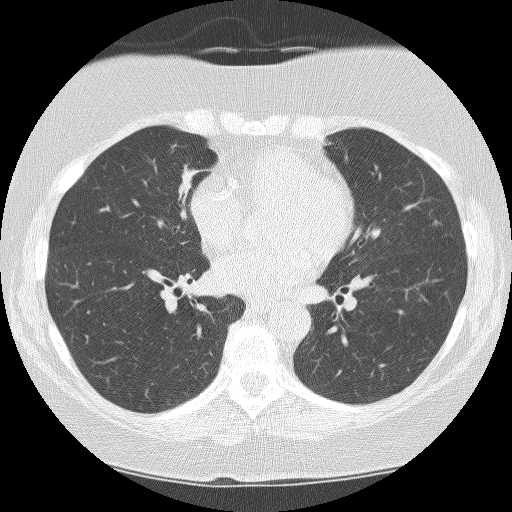
Low-dose screening chest CT, one axial slice; position 82 of 159 along the scan axis; 120 kVp; lung window (W 1500 / L -600 HU); 512 × 512 image matrix, field of view 299 × 299 mm.
Annotated regions visible in this slice (expert manual segmentation):
- lesion 1 (tumor, hilum of right lung): bounding box [x1, y1, x2, y2] px = [178, 163, 203, 203]